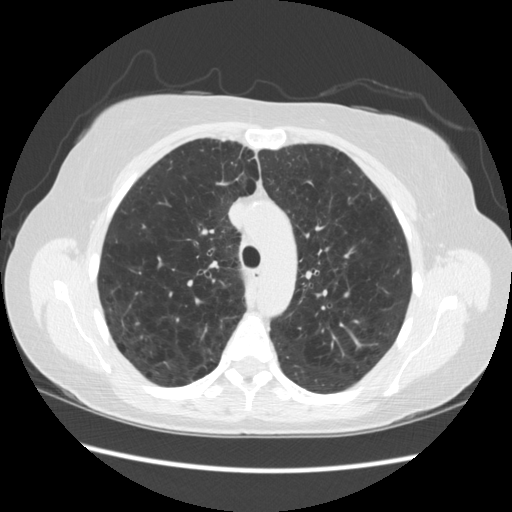
Low-dose screening chest CT, one axial slice; reconstruction kernel STANDARD; 120 kVp; lung window (W 1500 / L -600 HU); 2.5 mm slice thickness; 512 × 512 image matrix, field of view 360 × 360 mm.
Annotated regions visible in this slice (expert manual segmentation):
- lesion 1 (tumor, upper lobe of right lung): bounding box <201,344,216,363> (left, top, right, bottom; pixels)